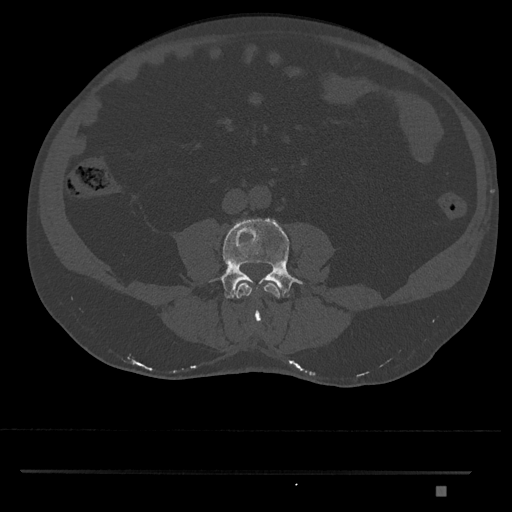
CT including the spine, one axial slice; position 636 of 1134 along the scan axis; reconstruction kernel Br40s/3; bone window (W 1800 / L 400 HU); 512 × 512 image matrix, field of view 429 × 429 mm. Patient: male, 65 years. Case-level facts recorded for this patient, not image findings: primary cancer: prostate.
Outlined on this slice (semi-automatically segmented with operator editing):
- L3 vertebra: bounding box [x1, y1, x2, y2] px = [236, 282, 280, 323]
- L4 vertebra: [211, 218, 303, 299]